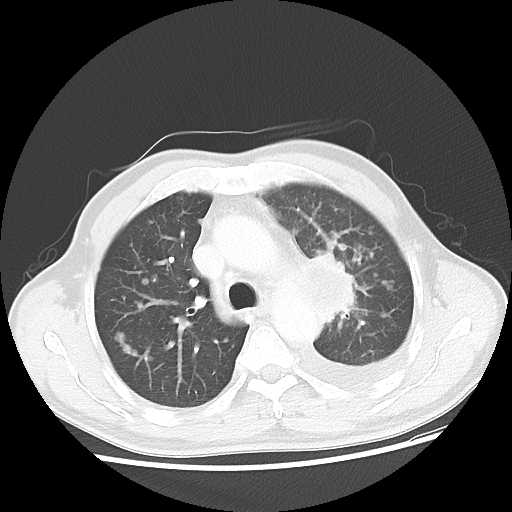
Chest CT, one axial slice; slice 32 of 47 in the series (ordered by position); 100 kVp; lung window (W 1500 / L -600 HU); 512 × 512 image matrix, field of view 362 × 362 mm. Male patient, age 55 years. From the clinical record (not read from this slice): clinical TNM (as recorded): T2 N3 M1a.
Annotated regions visible in this slice (rectangle marked by the reading radiologist):
- lung tumour (recorded histology: squamous cell carcinoma): bounding box <306,244,370,342> (left, top, right, bottom; pixels)